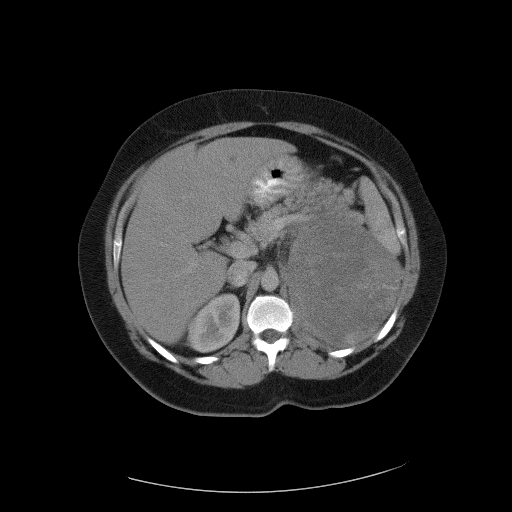
Contrast-enhanced abdominal CT, one axial slice. Slice 68 of 90 in the series (ordered by position). Reconstruction kernel FC01. 120 kVp. Intravenous contrast given. Soft-tissue window (W 400 / L 40 HU). 5 mm slice thickness. 512 × 512 image matrix. Female patient, age 55 years. From the clinical record (not read from this slice): diagnosis: adrenocortical carcinoma; tumour side: left adrenal; tumour size at pathology: 22 cm; Ki-67 index: 10 %; stage (as recorded): 3.
Structures marked on this image (semi-automatically segmented with operator editing):
- mass: bounding box <290,216,399,345> (left, top, right, bottom; pixels)